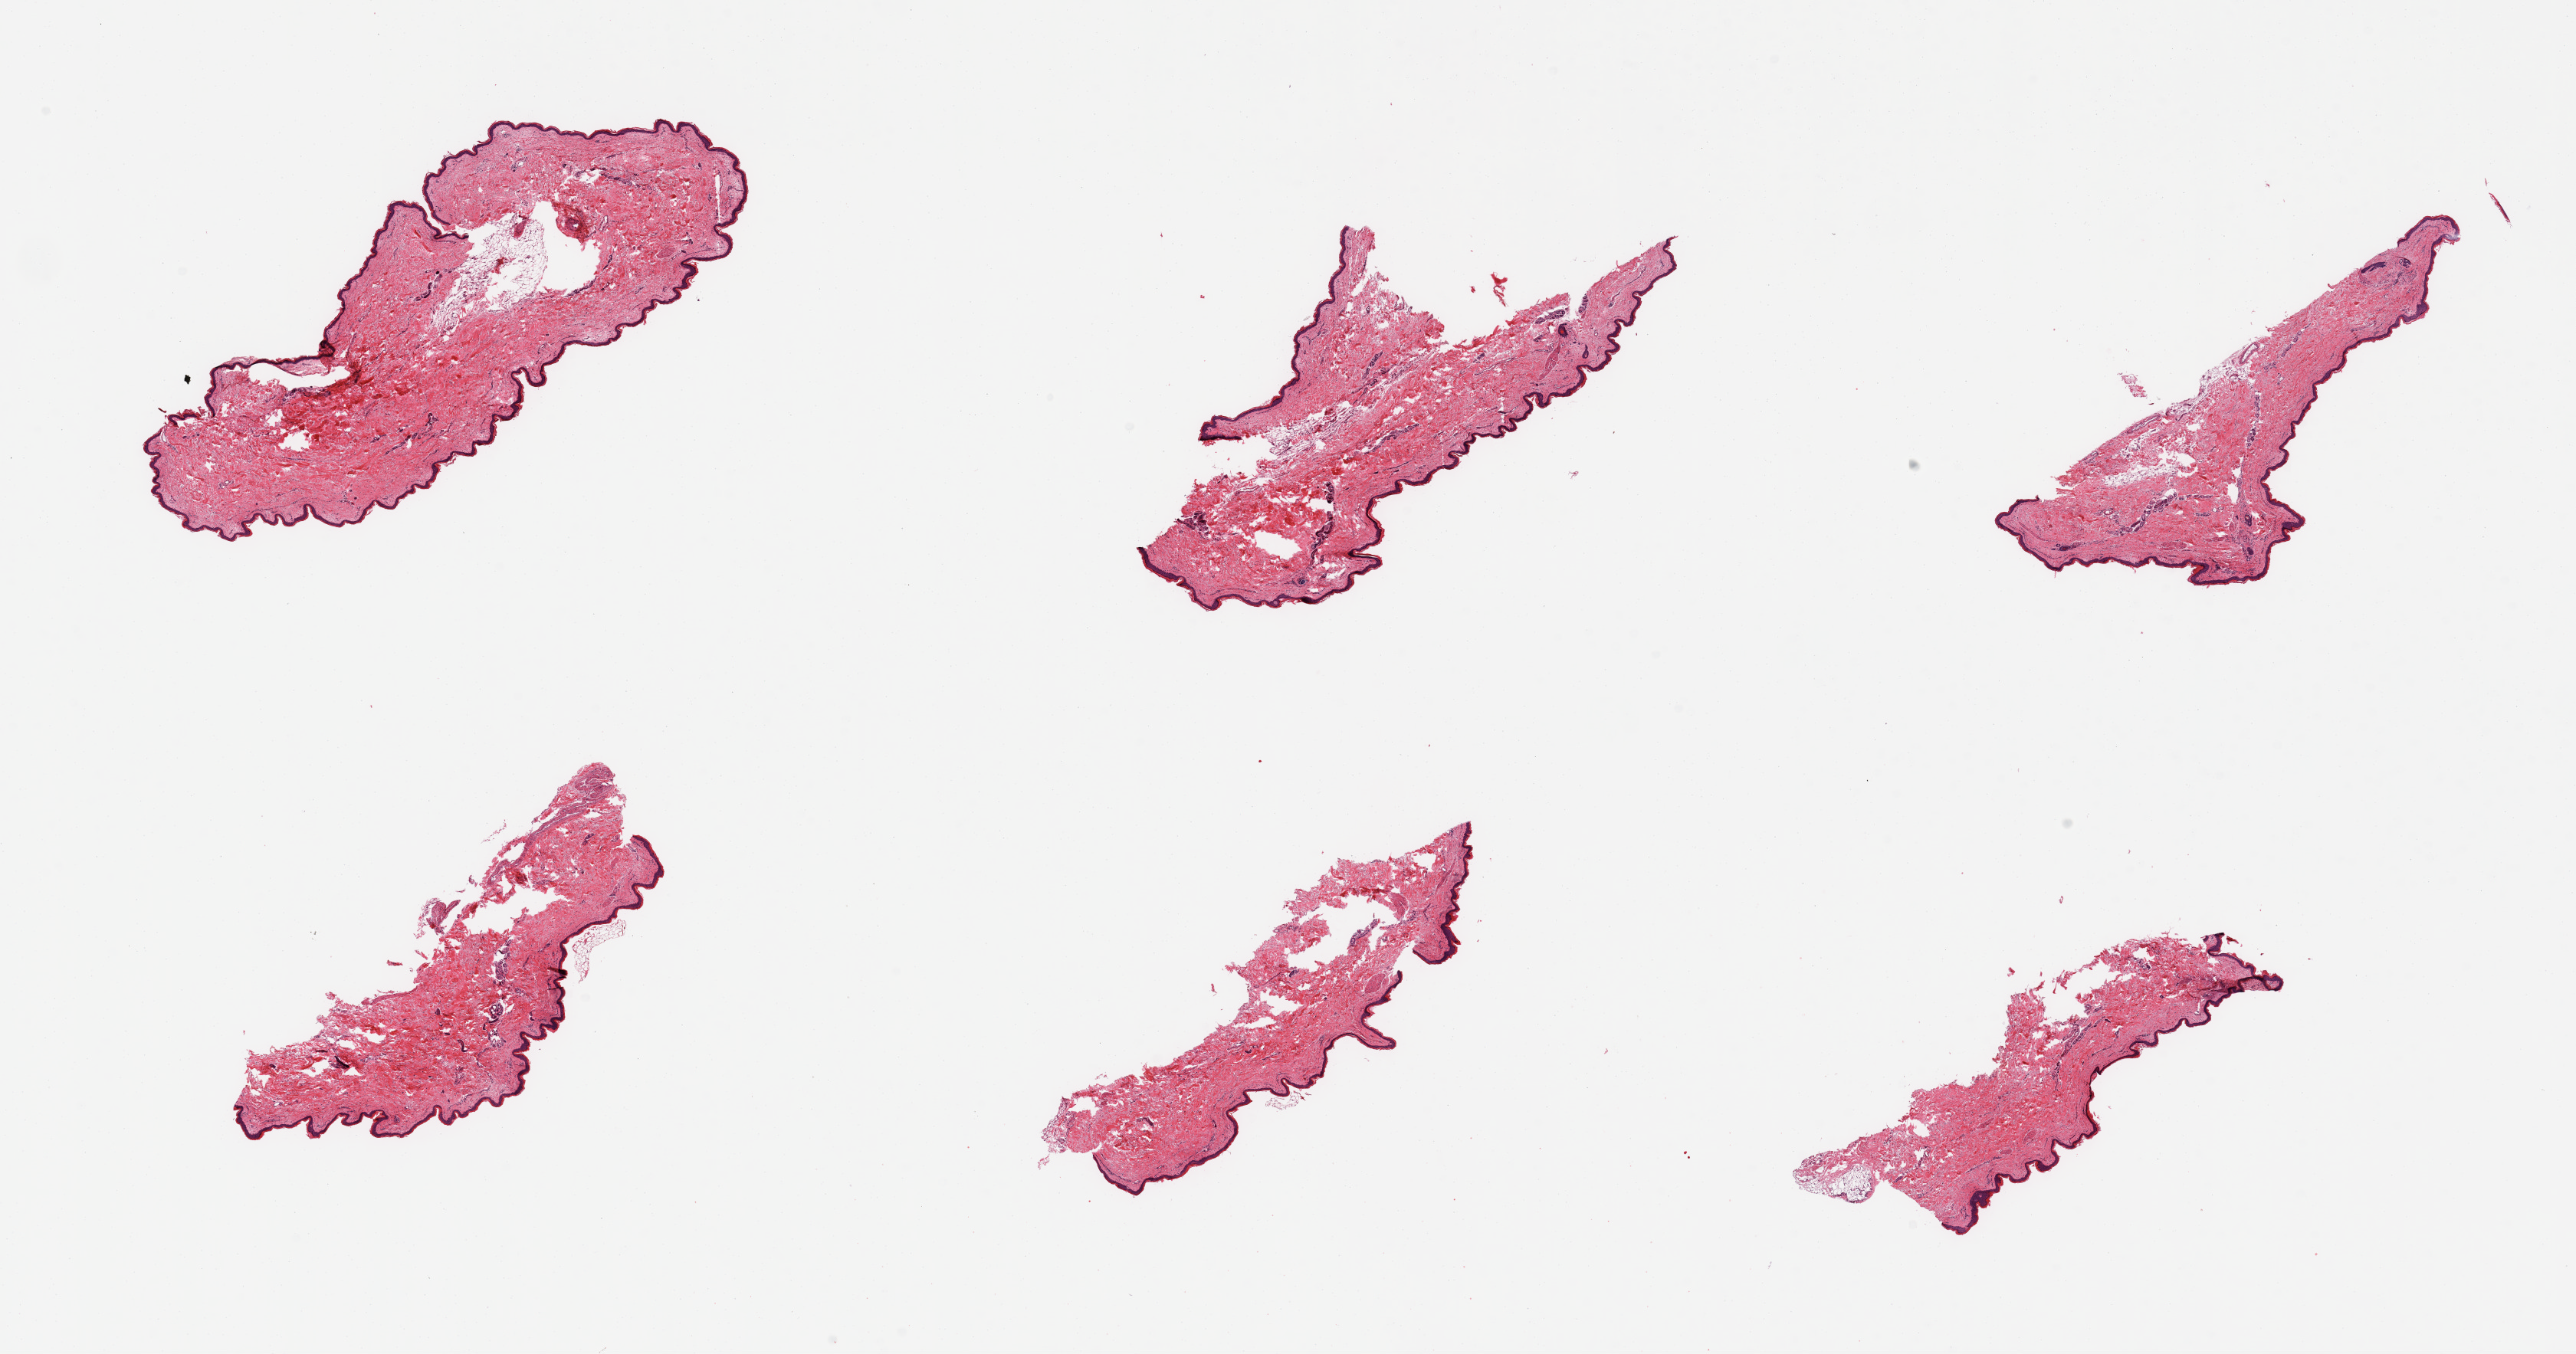
Digitized H&E-stained section, brightfield, shown as a low-resolution overview of the whole scanned area (about 26.6 x 14.0 mm), PAXgene-fixed paraffin-embedded (PFPE) section, target tissue: skin of lower leg, donor tissue sample. Donor sex: female.
- pathologist's review note for this sample: 6 pieces; well trimmed; minimal dermal fat